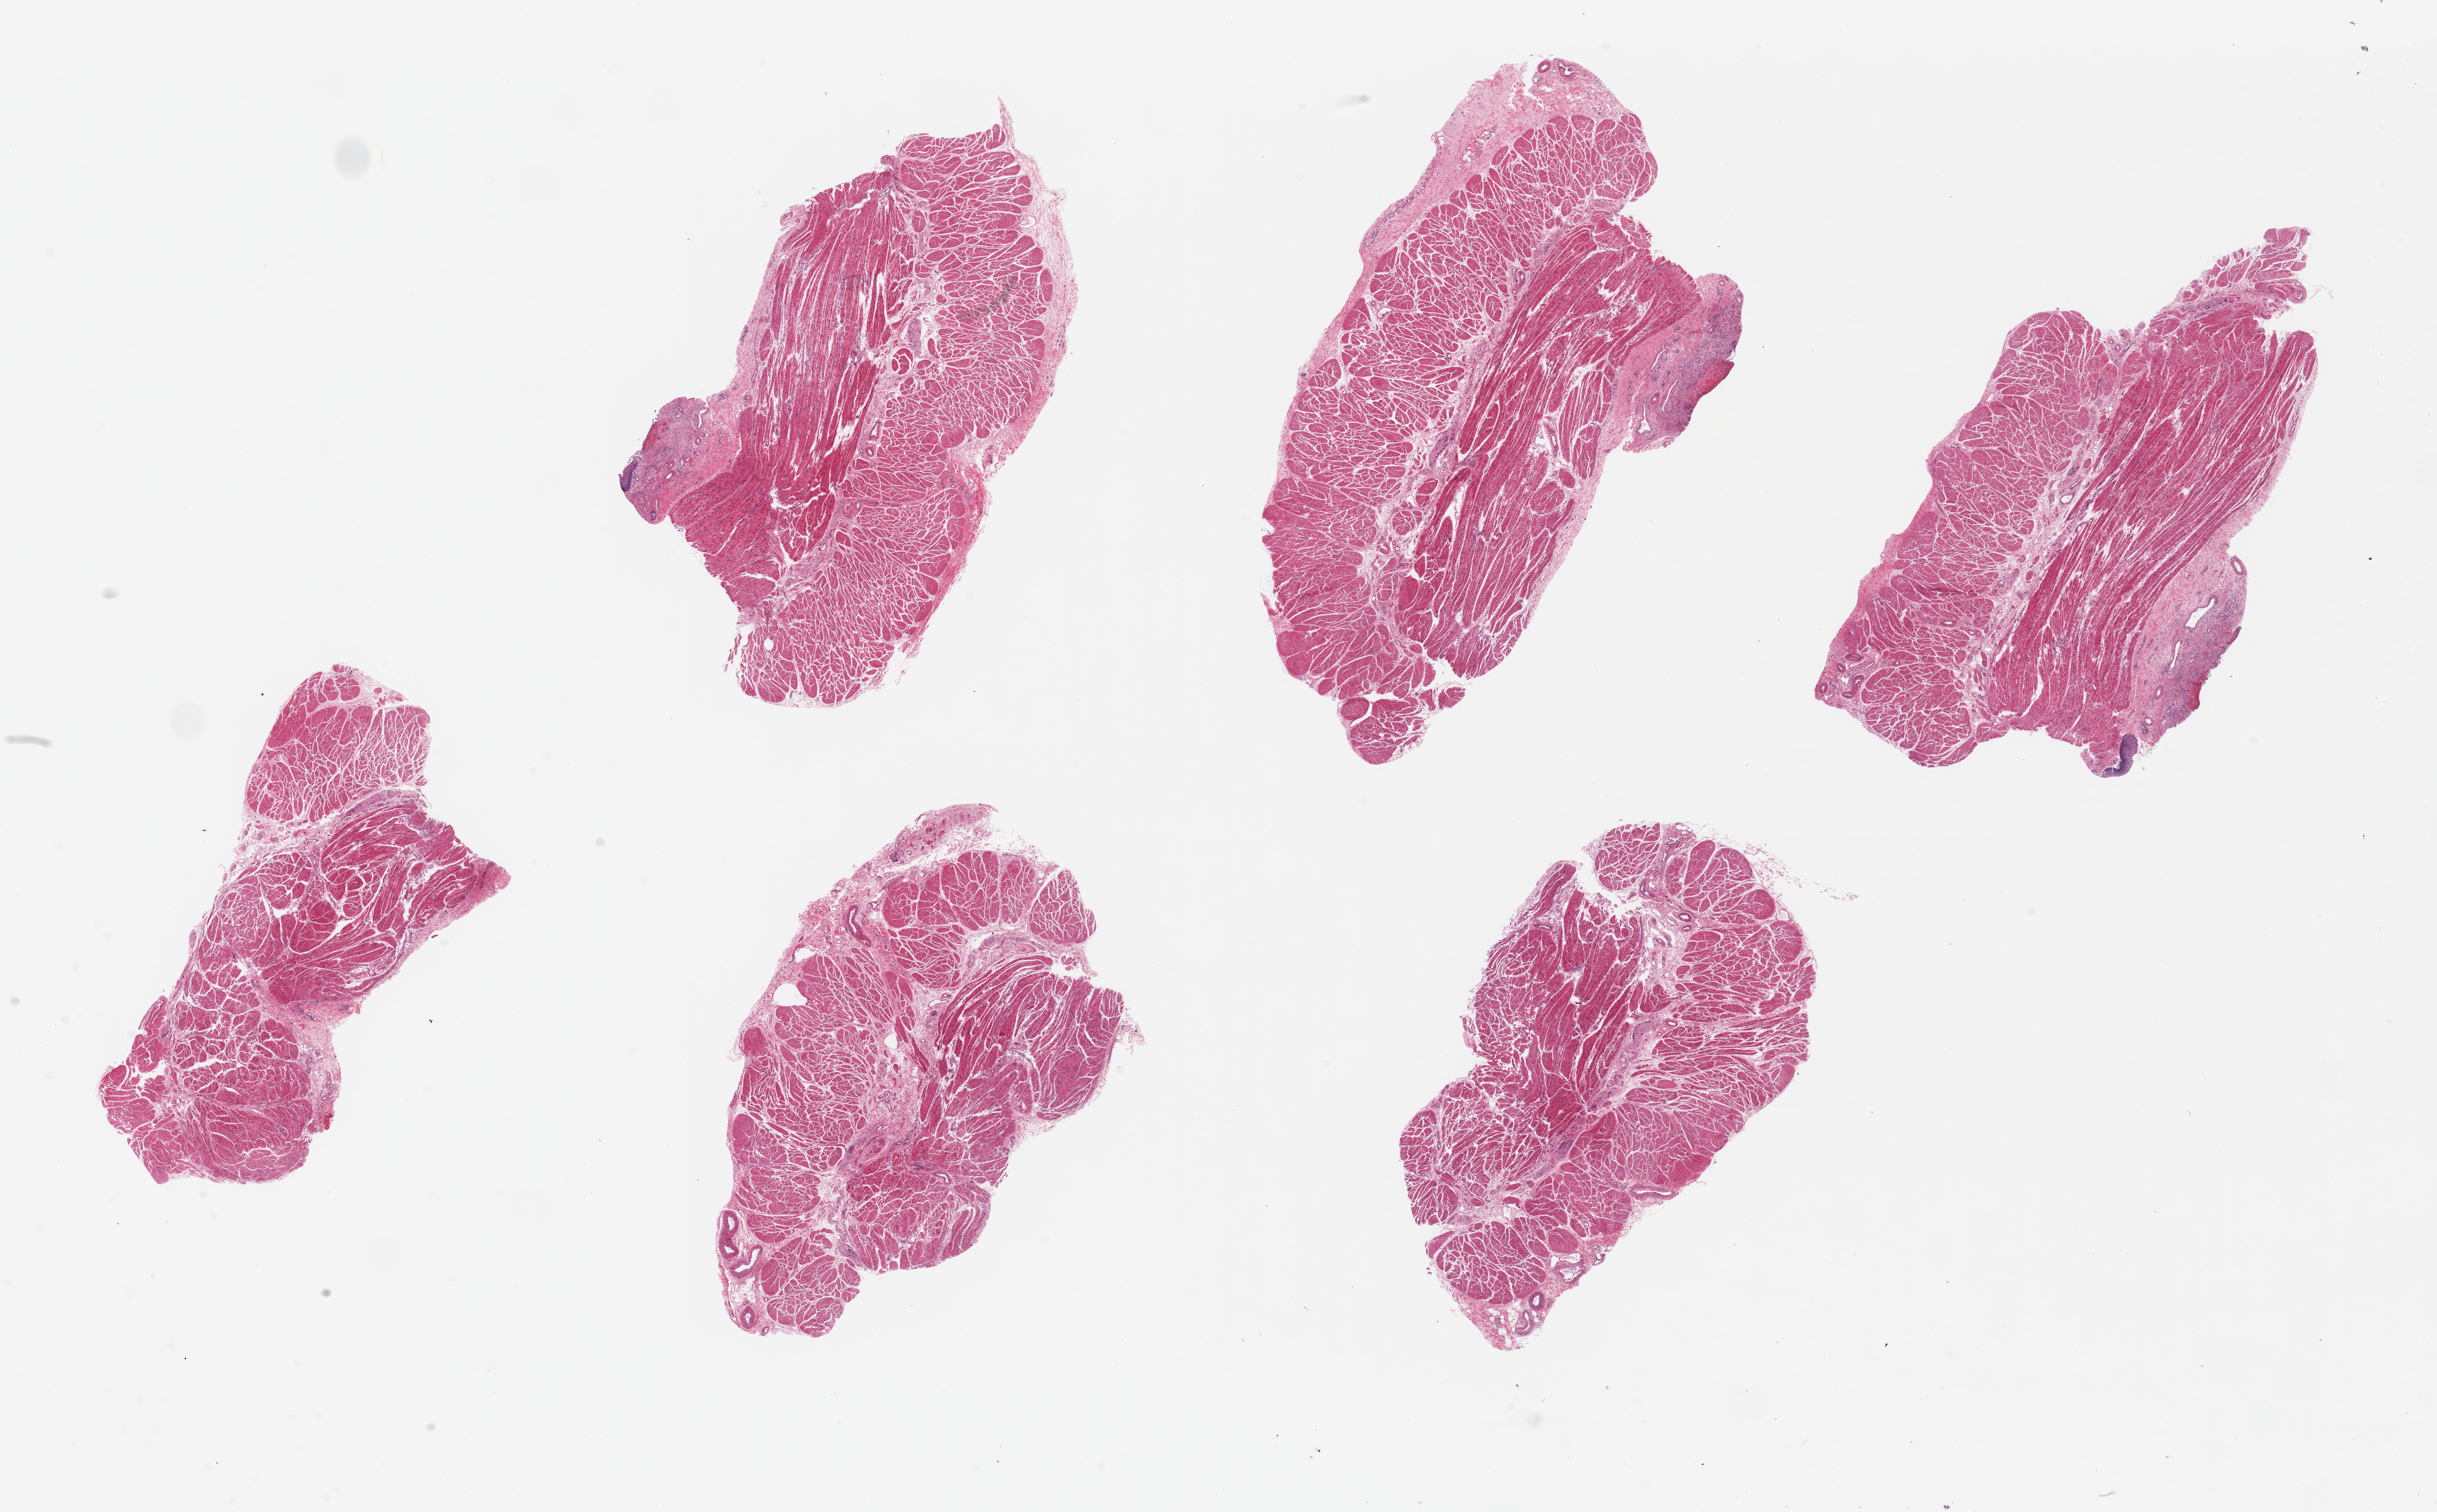
Digitized hematoxylin and eosin (H&E)-stained section — low-resolution overview of the scanned area, about 31.5 x 19.5 mm; PAXgene-fixed, paraffin-embedded tissue; target tissue: esophageal muscle; tissue donor sample. Donor: male.
- pathologist's review note for this sample: 6 pieces ~8x4mm, all muscularis, good specimens